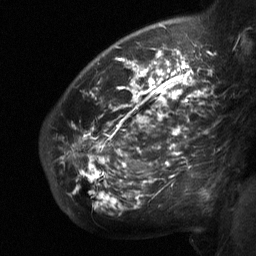
Breast MRI (dynamic contrast-enhanced), one sagittal slice; position 47 of 64 along the scan axis; dynamic contrast-enhanced study with each time point stored as its own series, time point 2 of 3 at this slice position (early post-contrast, ordered by acquisition time); 1.5 T; TE 4.8 ms, TR 27 ms; 2 mm slice thickness; 256 × 256 image matrix, field of view 200 × 200 mm. Patient: female, 50 years. Case-level facts recorded for this patient, not image findings: setting: breast cancer imaged before/during neoadjuvant chemotherapy; receptor status: HER2-positive.
Outlined on this slice (semi-automatic segmentation, software-assisted and operator-edited):
- analysis volume of interest (the breast-tissue region the enhancement analysis was run in; not a lesion): bounding box (x1, y1, x2, y2) in pixels: (49, 62, 212, 210)
- tumour enhancement mask (voxels above the 90 % enhancement threshold inside the analysis volume of interest): (81, 62, 205, 206)